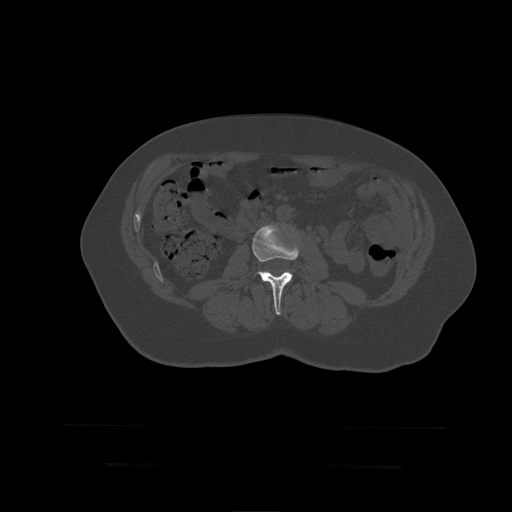
CT including the spine, one axial slice. Reconstruction kernel STANDARD. 120 kVp. Bone window (W 1800 / L 400 HU). 512 × 512 image matrix, field of view 450 × 450 mm. Patient age 41 years. Case-level facts recorded for this patient, not image findings: primary cancer: breast.
Outlined on this slice (semi-automatically segmented with operator editing):
- L3 vertebra: bounding box (x1, y1, x2, y2) in pixels: (252, 224, 300, 315)